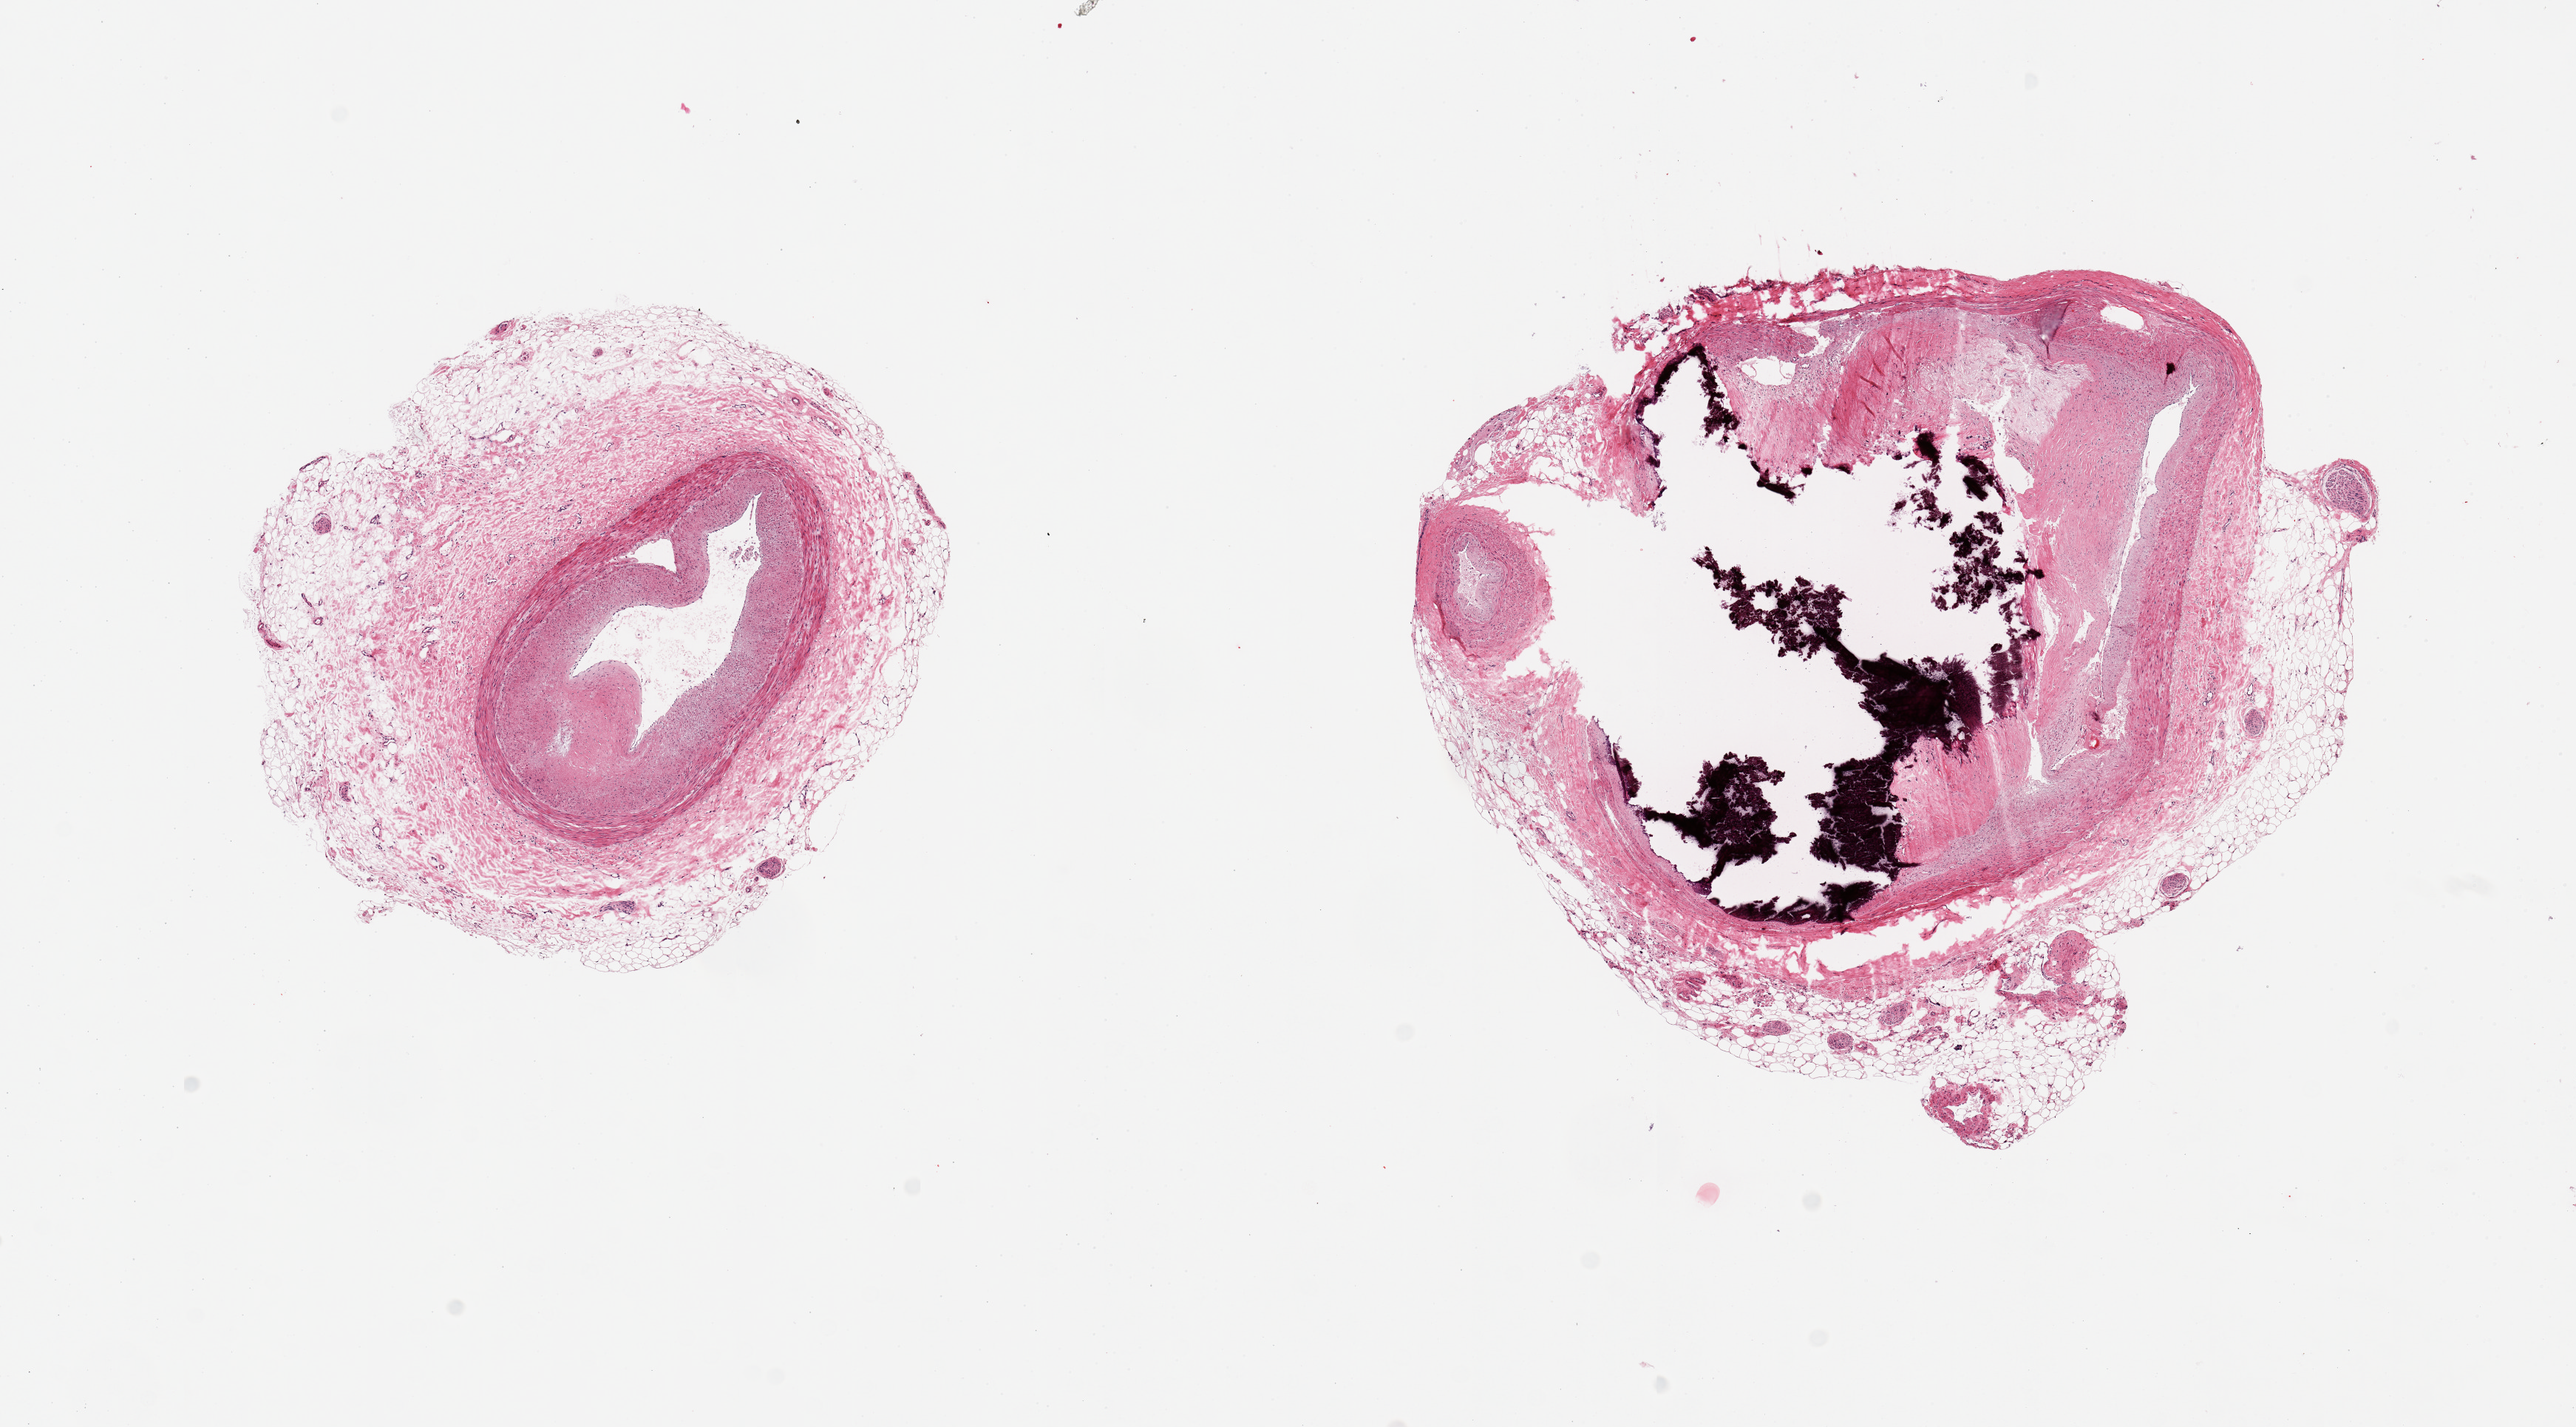
Digitized H&E-stained section, low-resolution overview of the scanned area, about 13.8 x 7.6 mm (slide scanned at 20x), PAXgene-fixed paraffin-embedded (PFPE) section, target tissue: coronary artery, tissue donor sample. Female donor.
Review note (as recorded): 2 pieces; 1 with focal plaque & 1mm external fibrofatty collar; 1 with large (2.6 mm) calcified plaque.